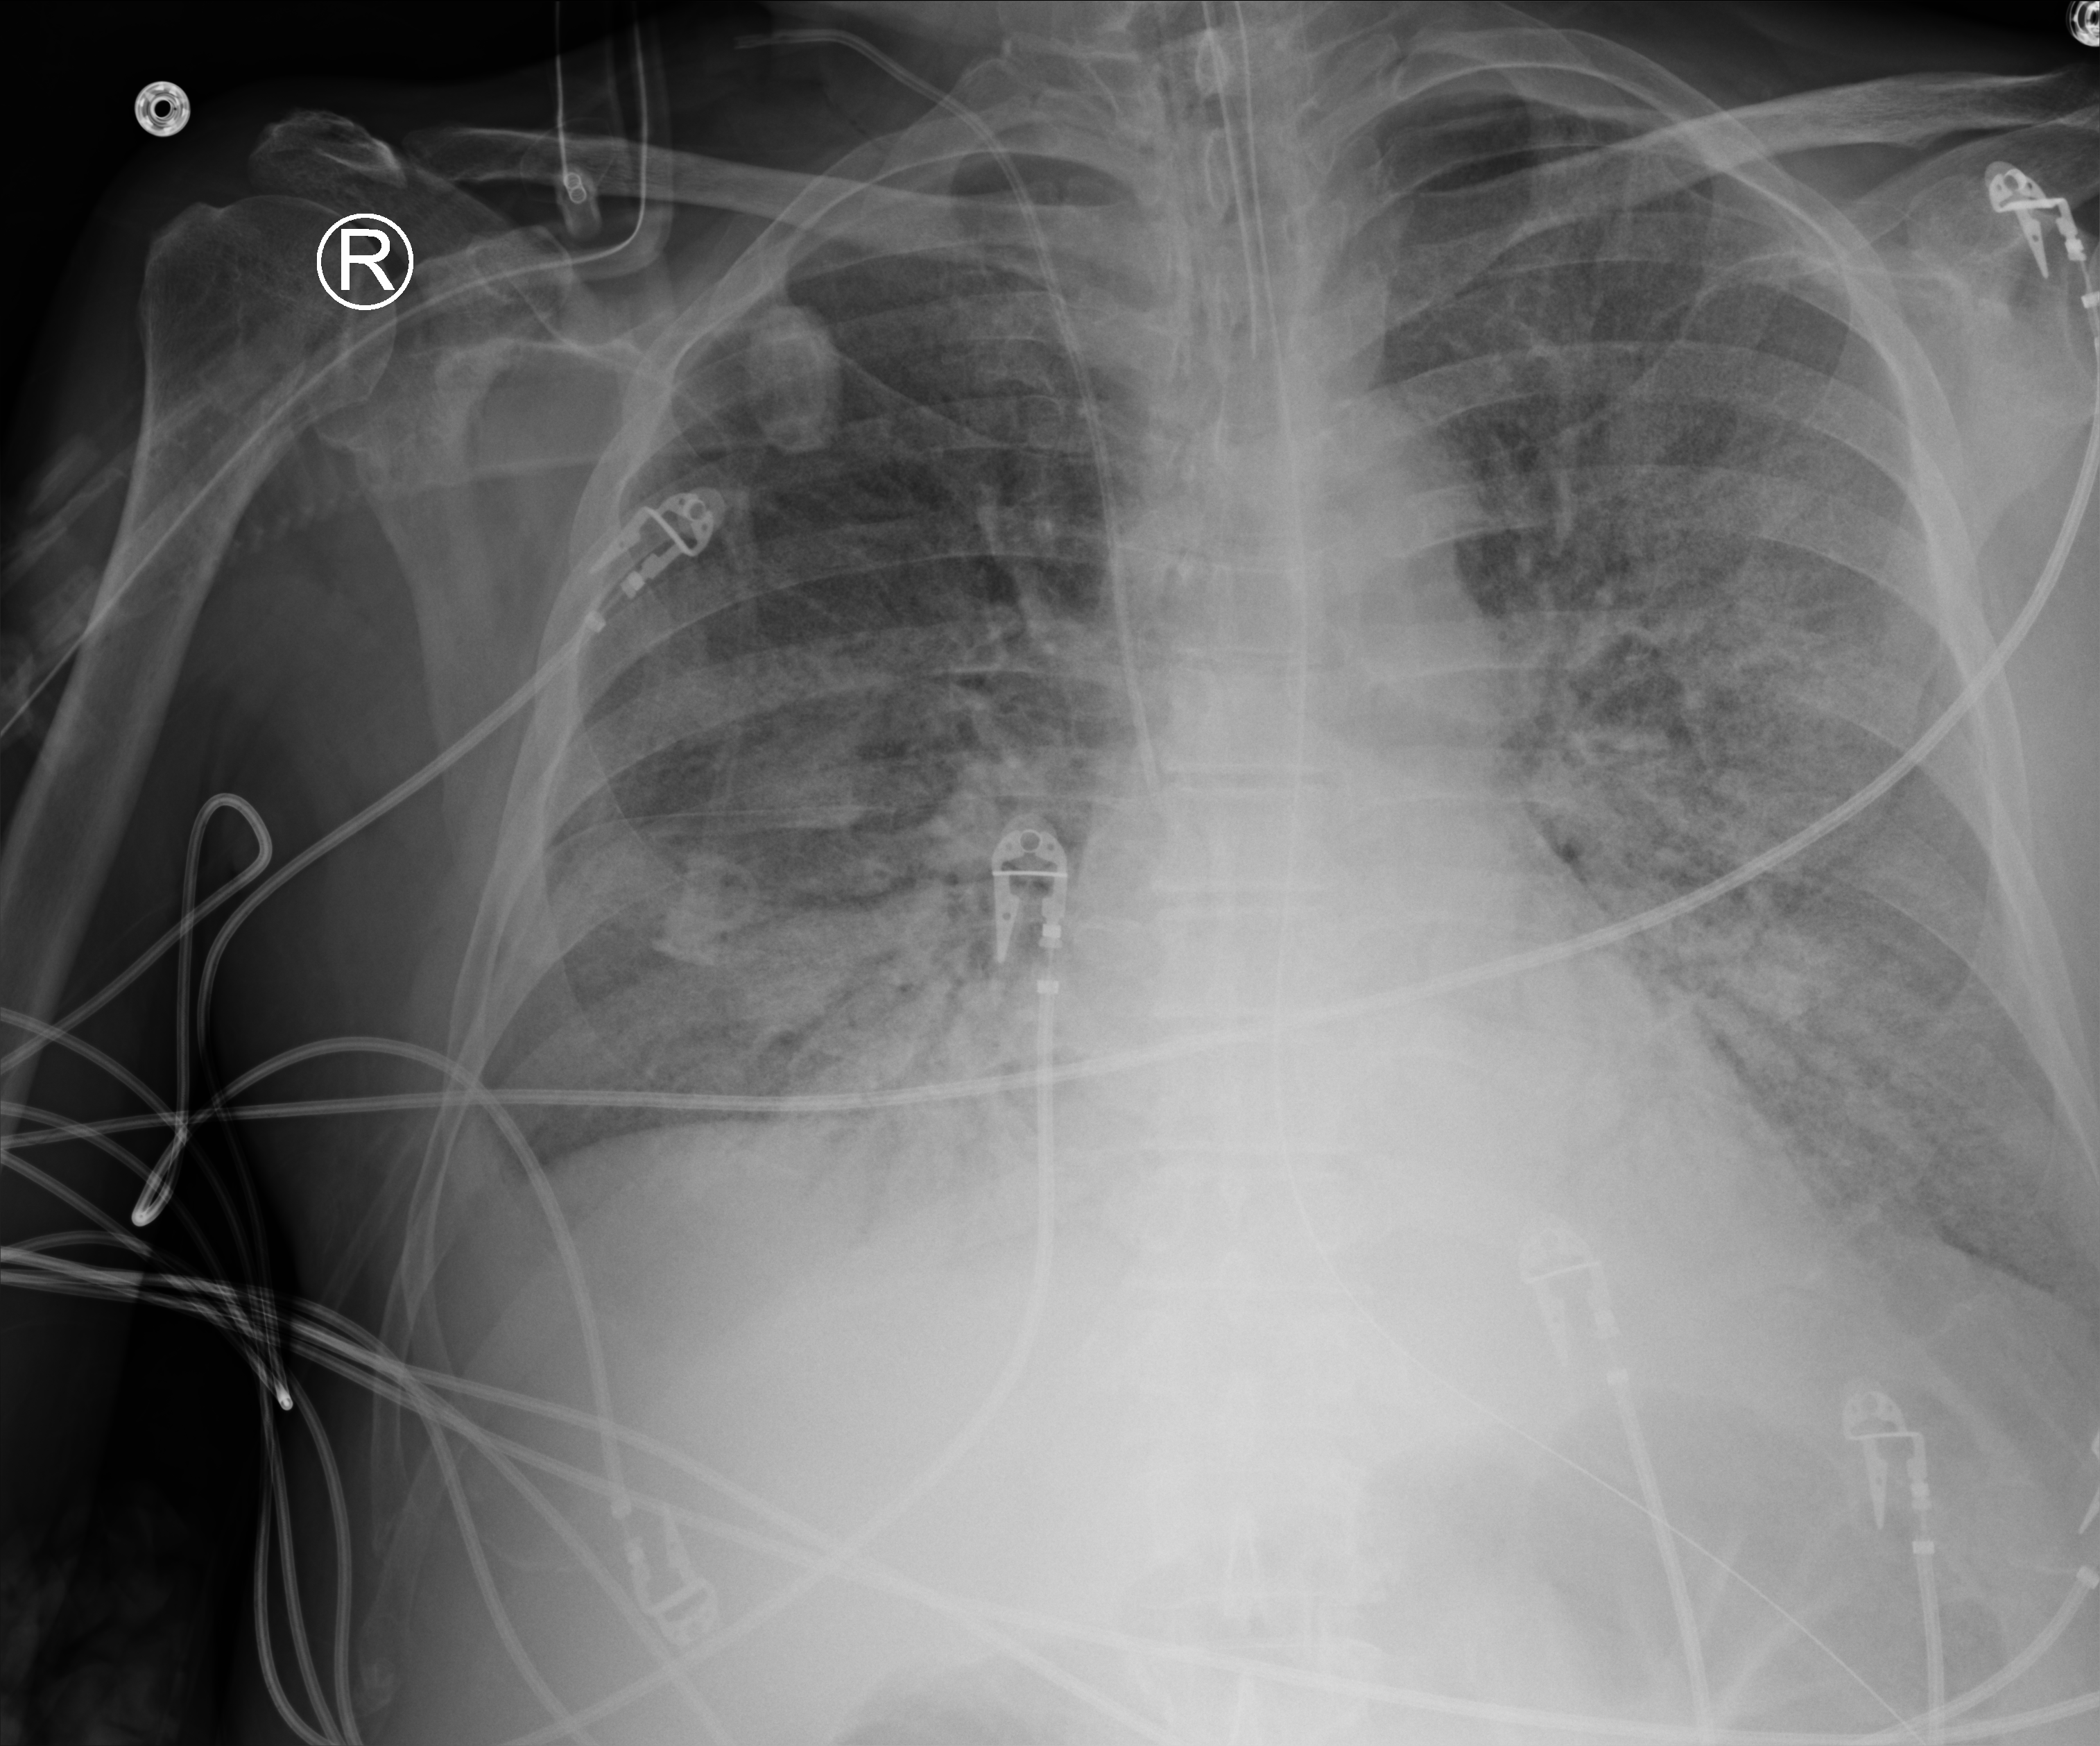
Portable chest radiograph, anteroposterior (AP) projection. Patient hospitalised with COVID-19; male, aged 60–74 years.
Hospital-stay facts (about this admission, not read from this image; timing relative to this image not recorded): diabetes (admission record): yes.